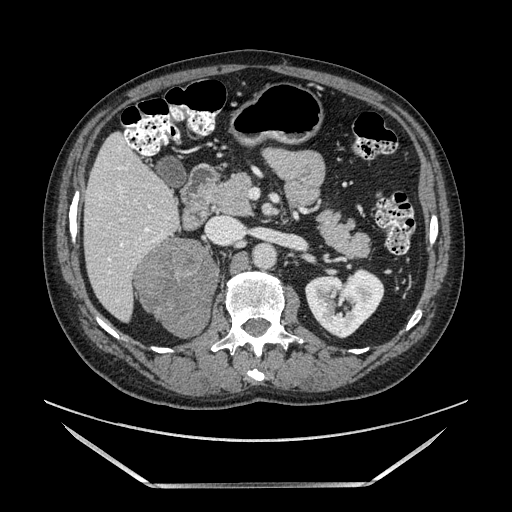
Contrast-enhanced abdominal CT, one axial slice; position 65 of 185 along the scan axis; soft-tissue window (W 400 / L 40 HU); 1.25 mm slice thickness; 512 × 512 image matrix, field of view 440 × 440 mm. Male patient. Case-level facts recorded for this patient, not image findings: diagnosis: adrenocortical carcinoma; tumour side: right adrenal; tumour size at pathology: 10.3 cm; Ki-67 index: 20 %; stage (as recorded): 3.
Structures marked on this image (semi-automatically segmented with operator editing):
- mass: bounding box [x1, y1, x2, y2] px = [138, 240, 215, 338]